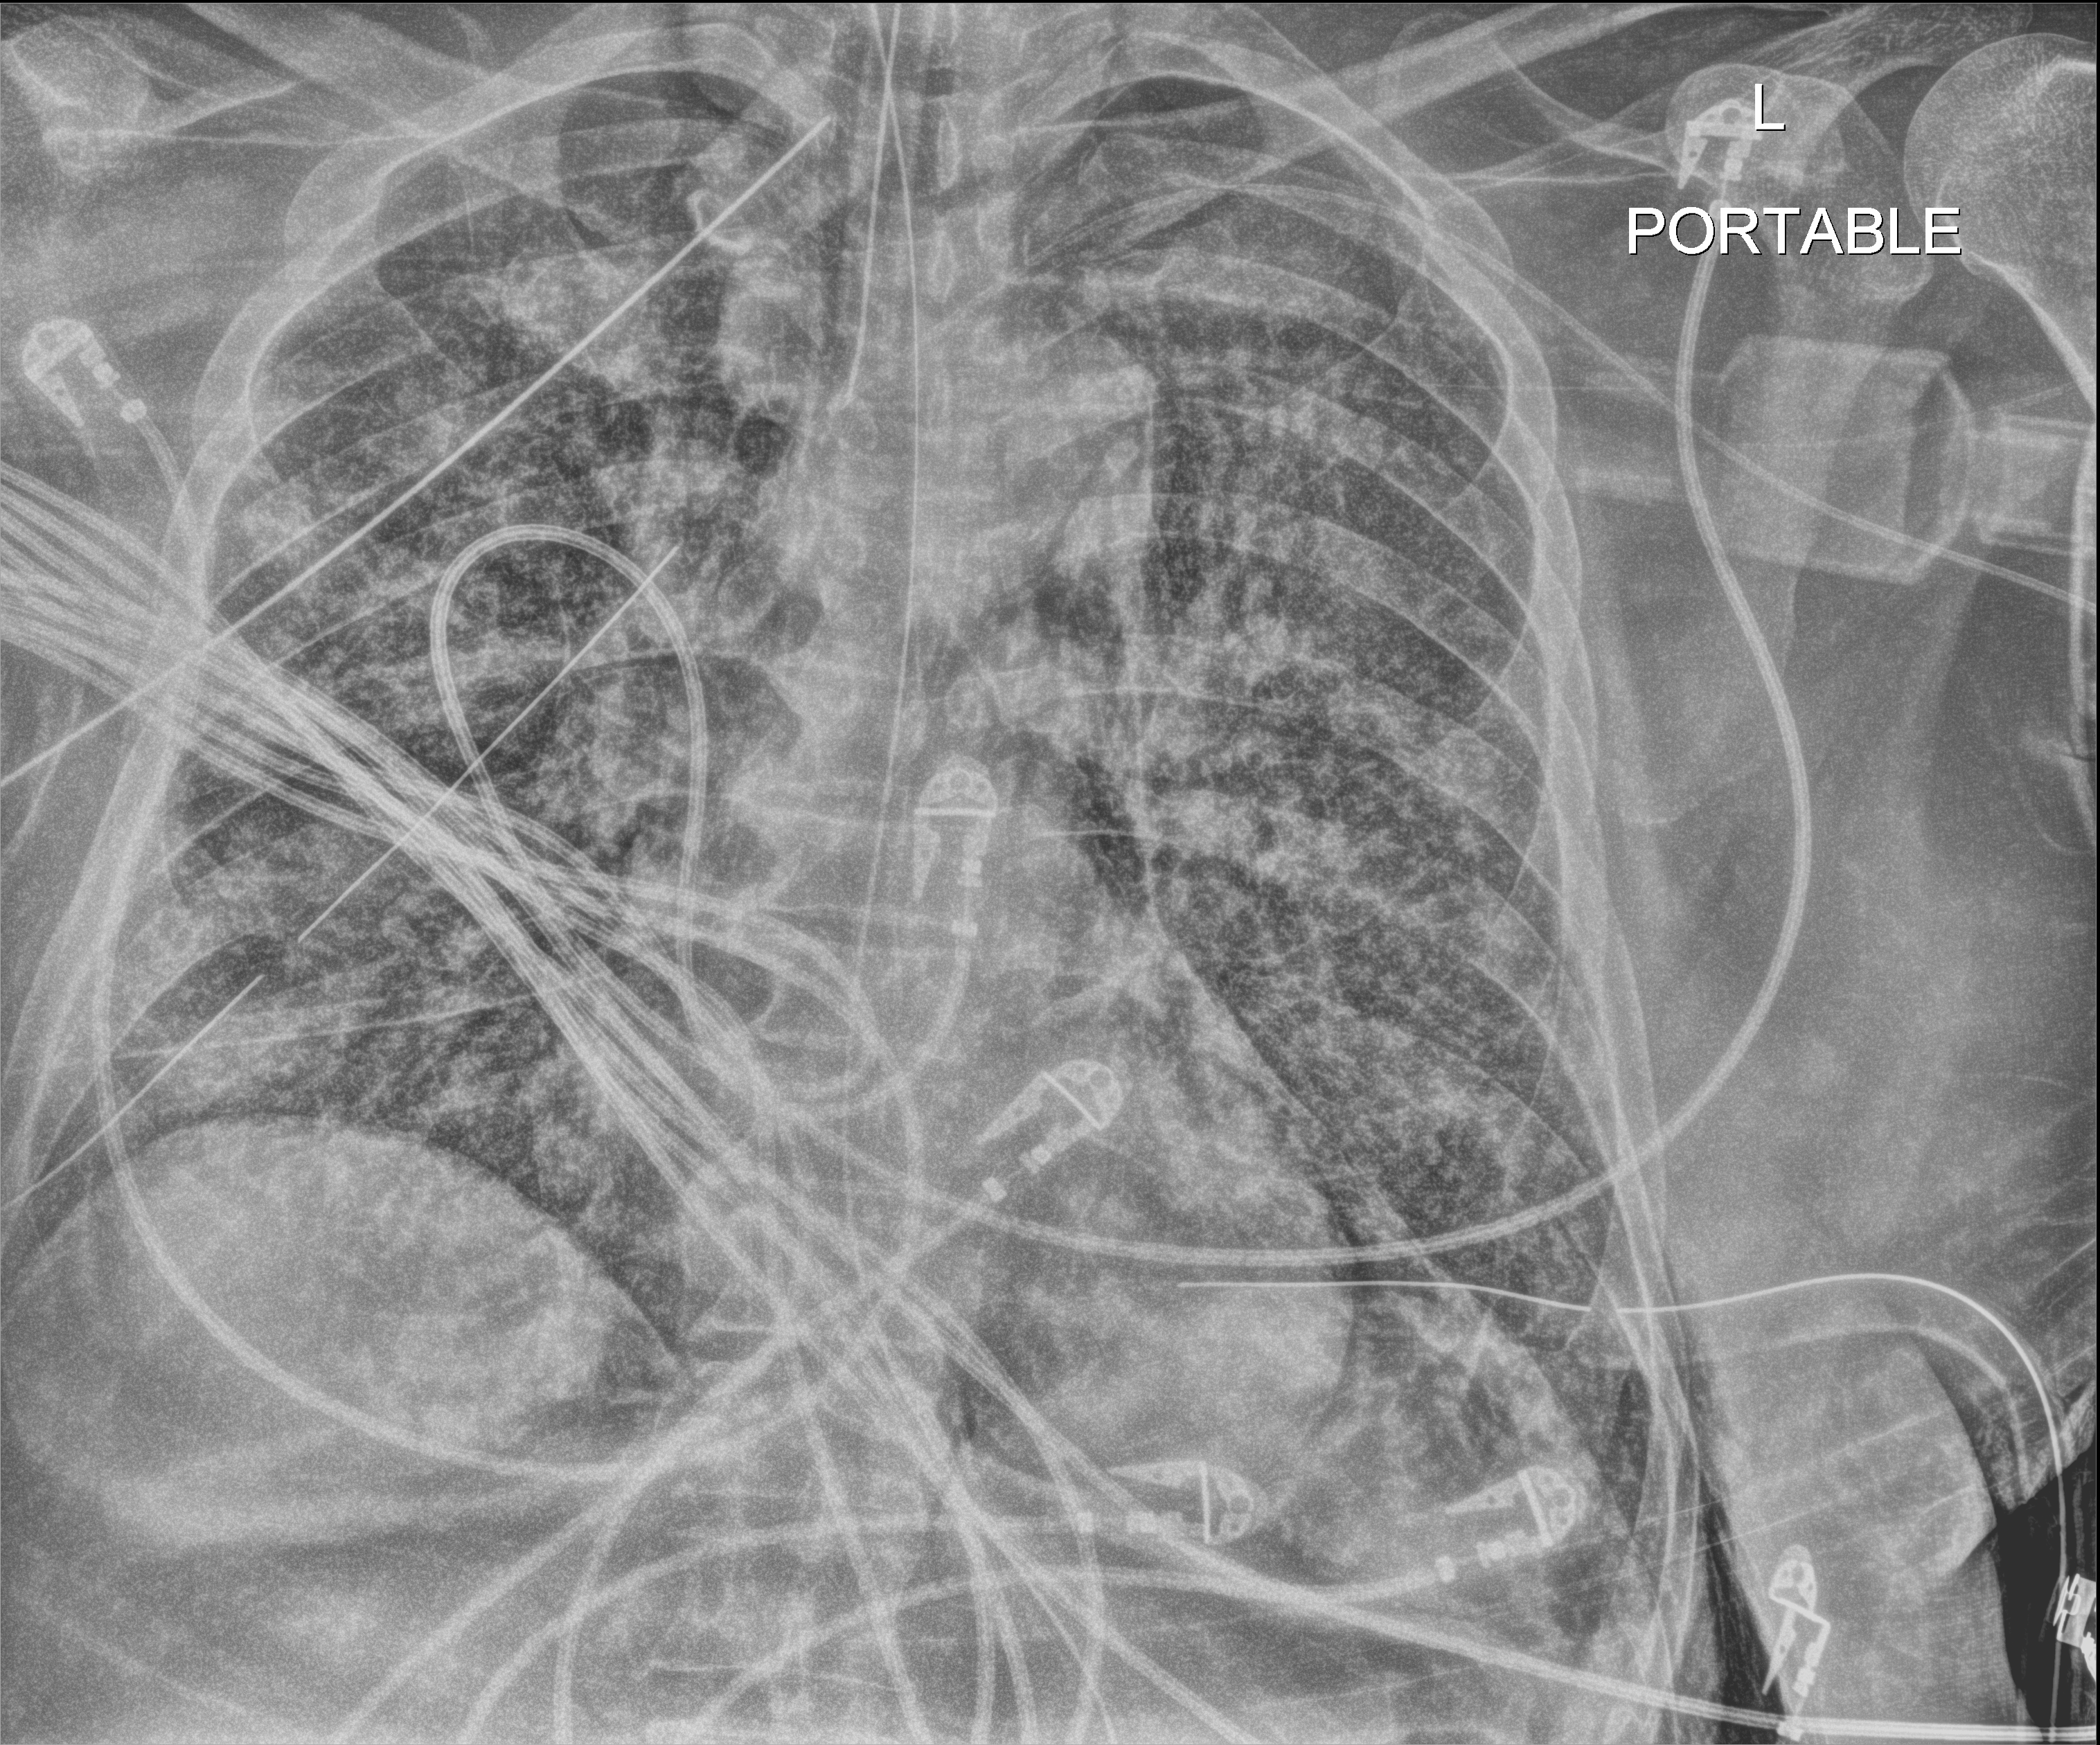
Chest radiograph, anteroposterior (AP) projection. Adult patient hospitalised with COVID-19, age 18–59 years.
Admission-level facts for this patient (not findings on this image; timing relative to this image not recorded):
- admitted to intensive care during this hospital stay: yes
- mechanically ventilated during this hospital stay: yes